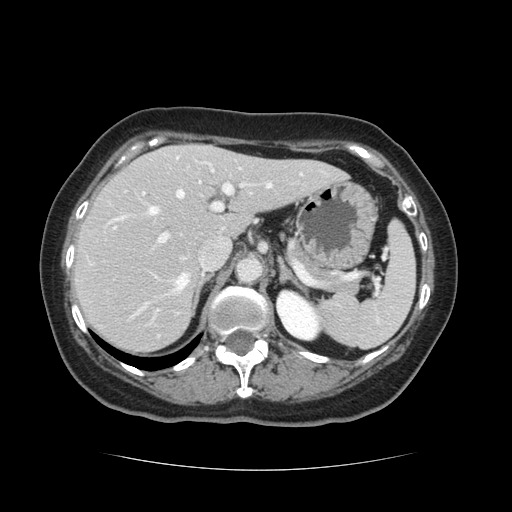
Contrast-enhanced abdominal CT, one axial slice. Slice 82 of 128 in the series (ordered by position). 120 kVp. Intravenous contrast given. Soft-tissue window (W 400 / L 40 HU). 2.5 mm slice thickness. 512 × 512 image matrix, field of view 366 × 366 mm. Female patient, age 67 years. From the clinical record (not read from this slice): diagnosis: colorectal cancer liver metastases, imaged before liver resection; multiple liver metastases: yes; largest metastasis: 3 cm.
Annotated regions visible in this slice (expert manual segmentation):
- hepatic veins: bounding box [x1, y1, x2, y2] px = [121, 184, 272, 309]
- liver: [74, 145, 343, 353]
- planned liver remnant (the part of the liver to remain after resection): [73, 157, 343, 353]
- portal vein (with intrahepatic branches): [144, 159, 253, 243]